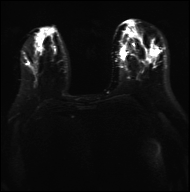
Breast MRI, one axial slice. Position 11 of 36 along the scan axis. Diffusion-weighted series; image 2 of 4 stored at this slice position (different b-values; order by instance number). 3 T. 4 mm slice thickness. 190 × 192 image matrix, field of view 317 × 320 mm. Female patient.
Structures marked on this image (expert manual segmentation):
- tumour on diffusion-weighted imaging: bounding box [x1, y1, x2, y2] px = [49, 48, 61, 54]